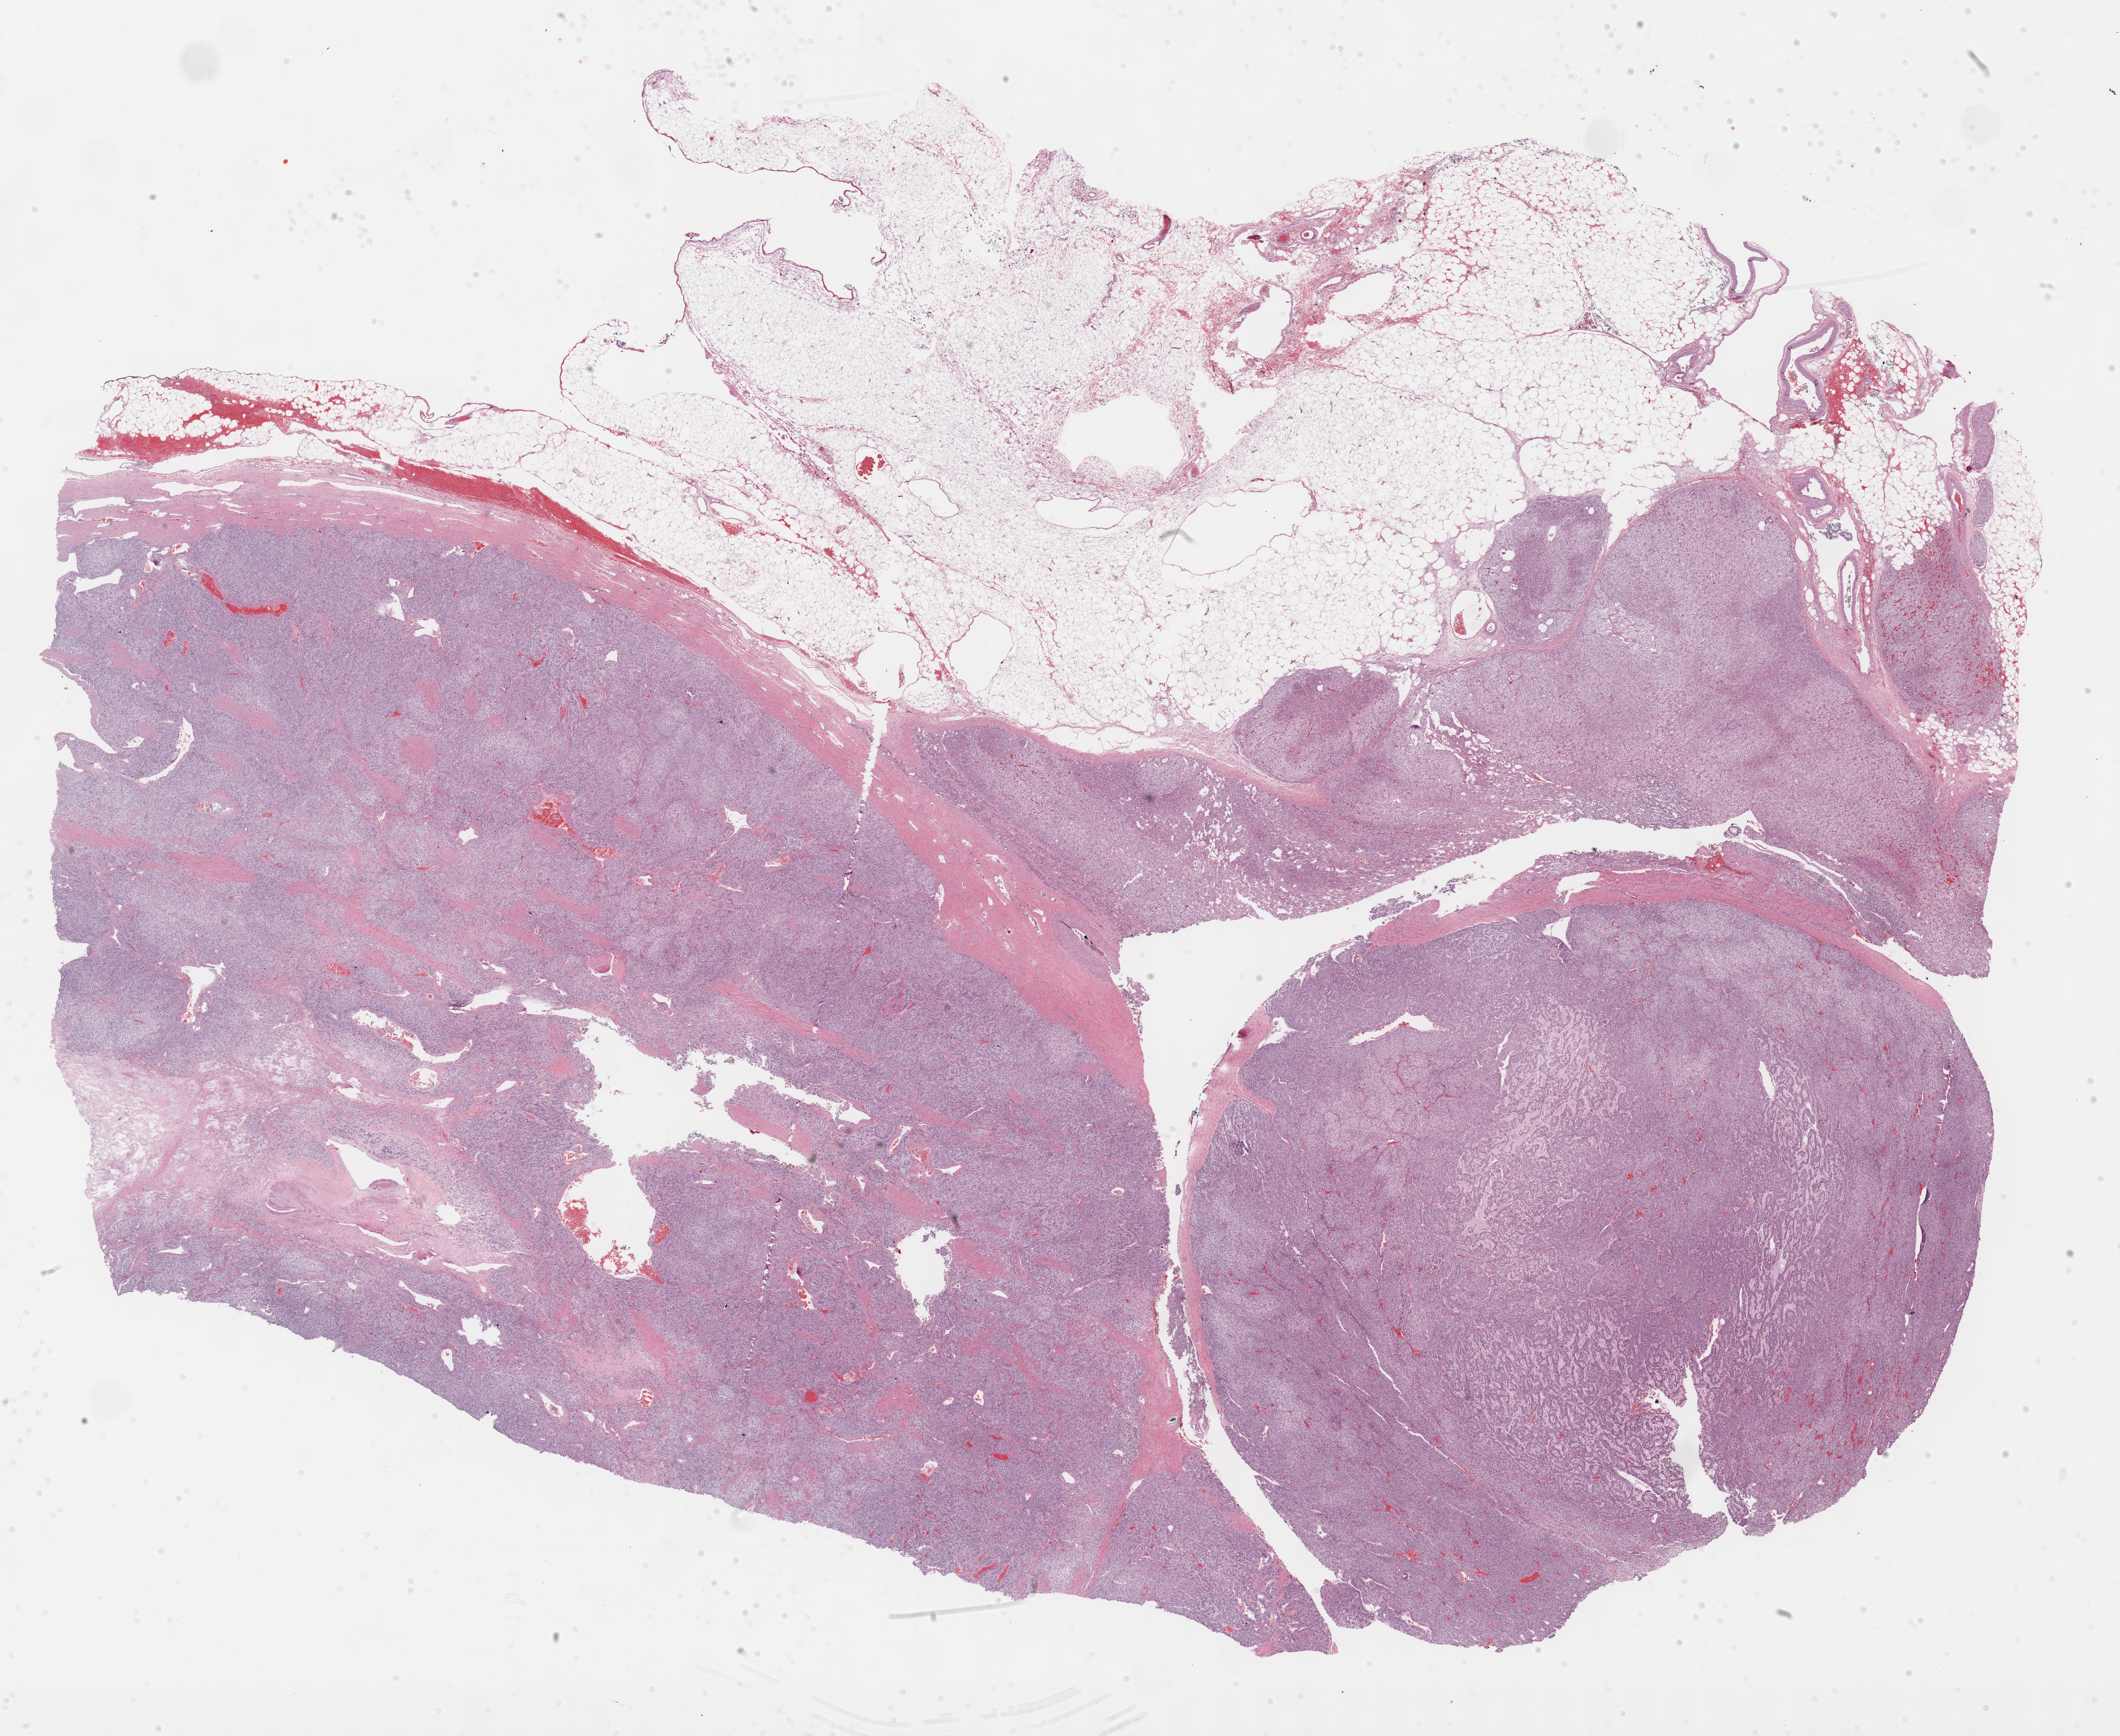
H&E-stained whole-slide image, low-resolution overview of the scanned area, about 25.7 x 21.0 mm (from a 40x scan), formalin-fixed paraffin-embedded (FFPE) diagnostic section, adrenal cortex, primary tumour sample. Male, age 50 years at initial diagnosis.
• pathologic diagnosis: Adrenal cortical carcinoma (cortex of adrenal gland)
• lymph nodes positive (case pathology): 0 of 1 examined